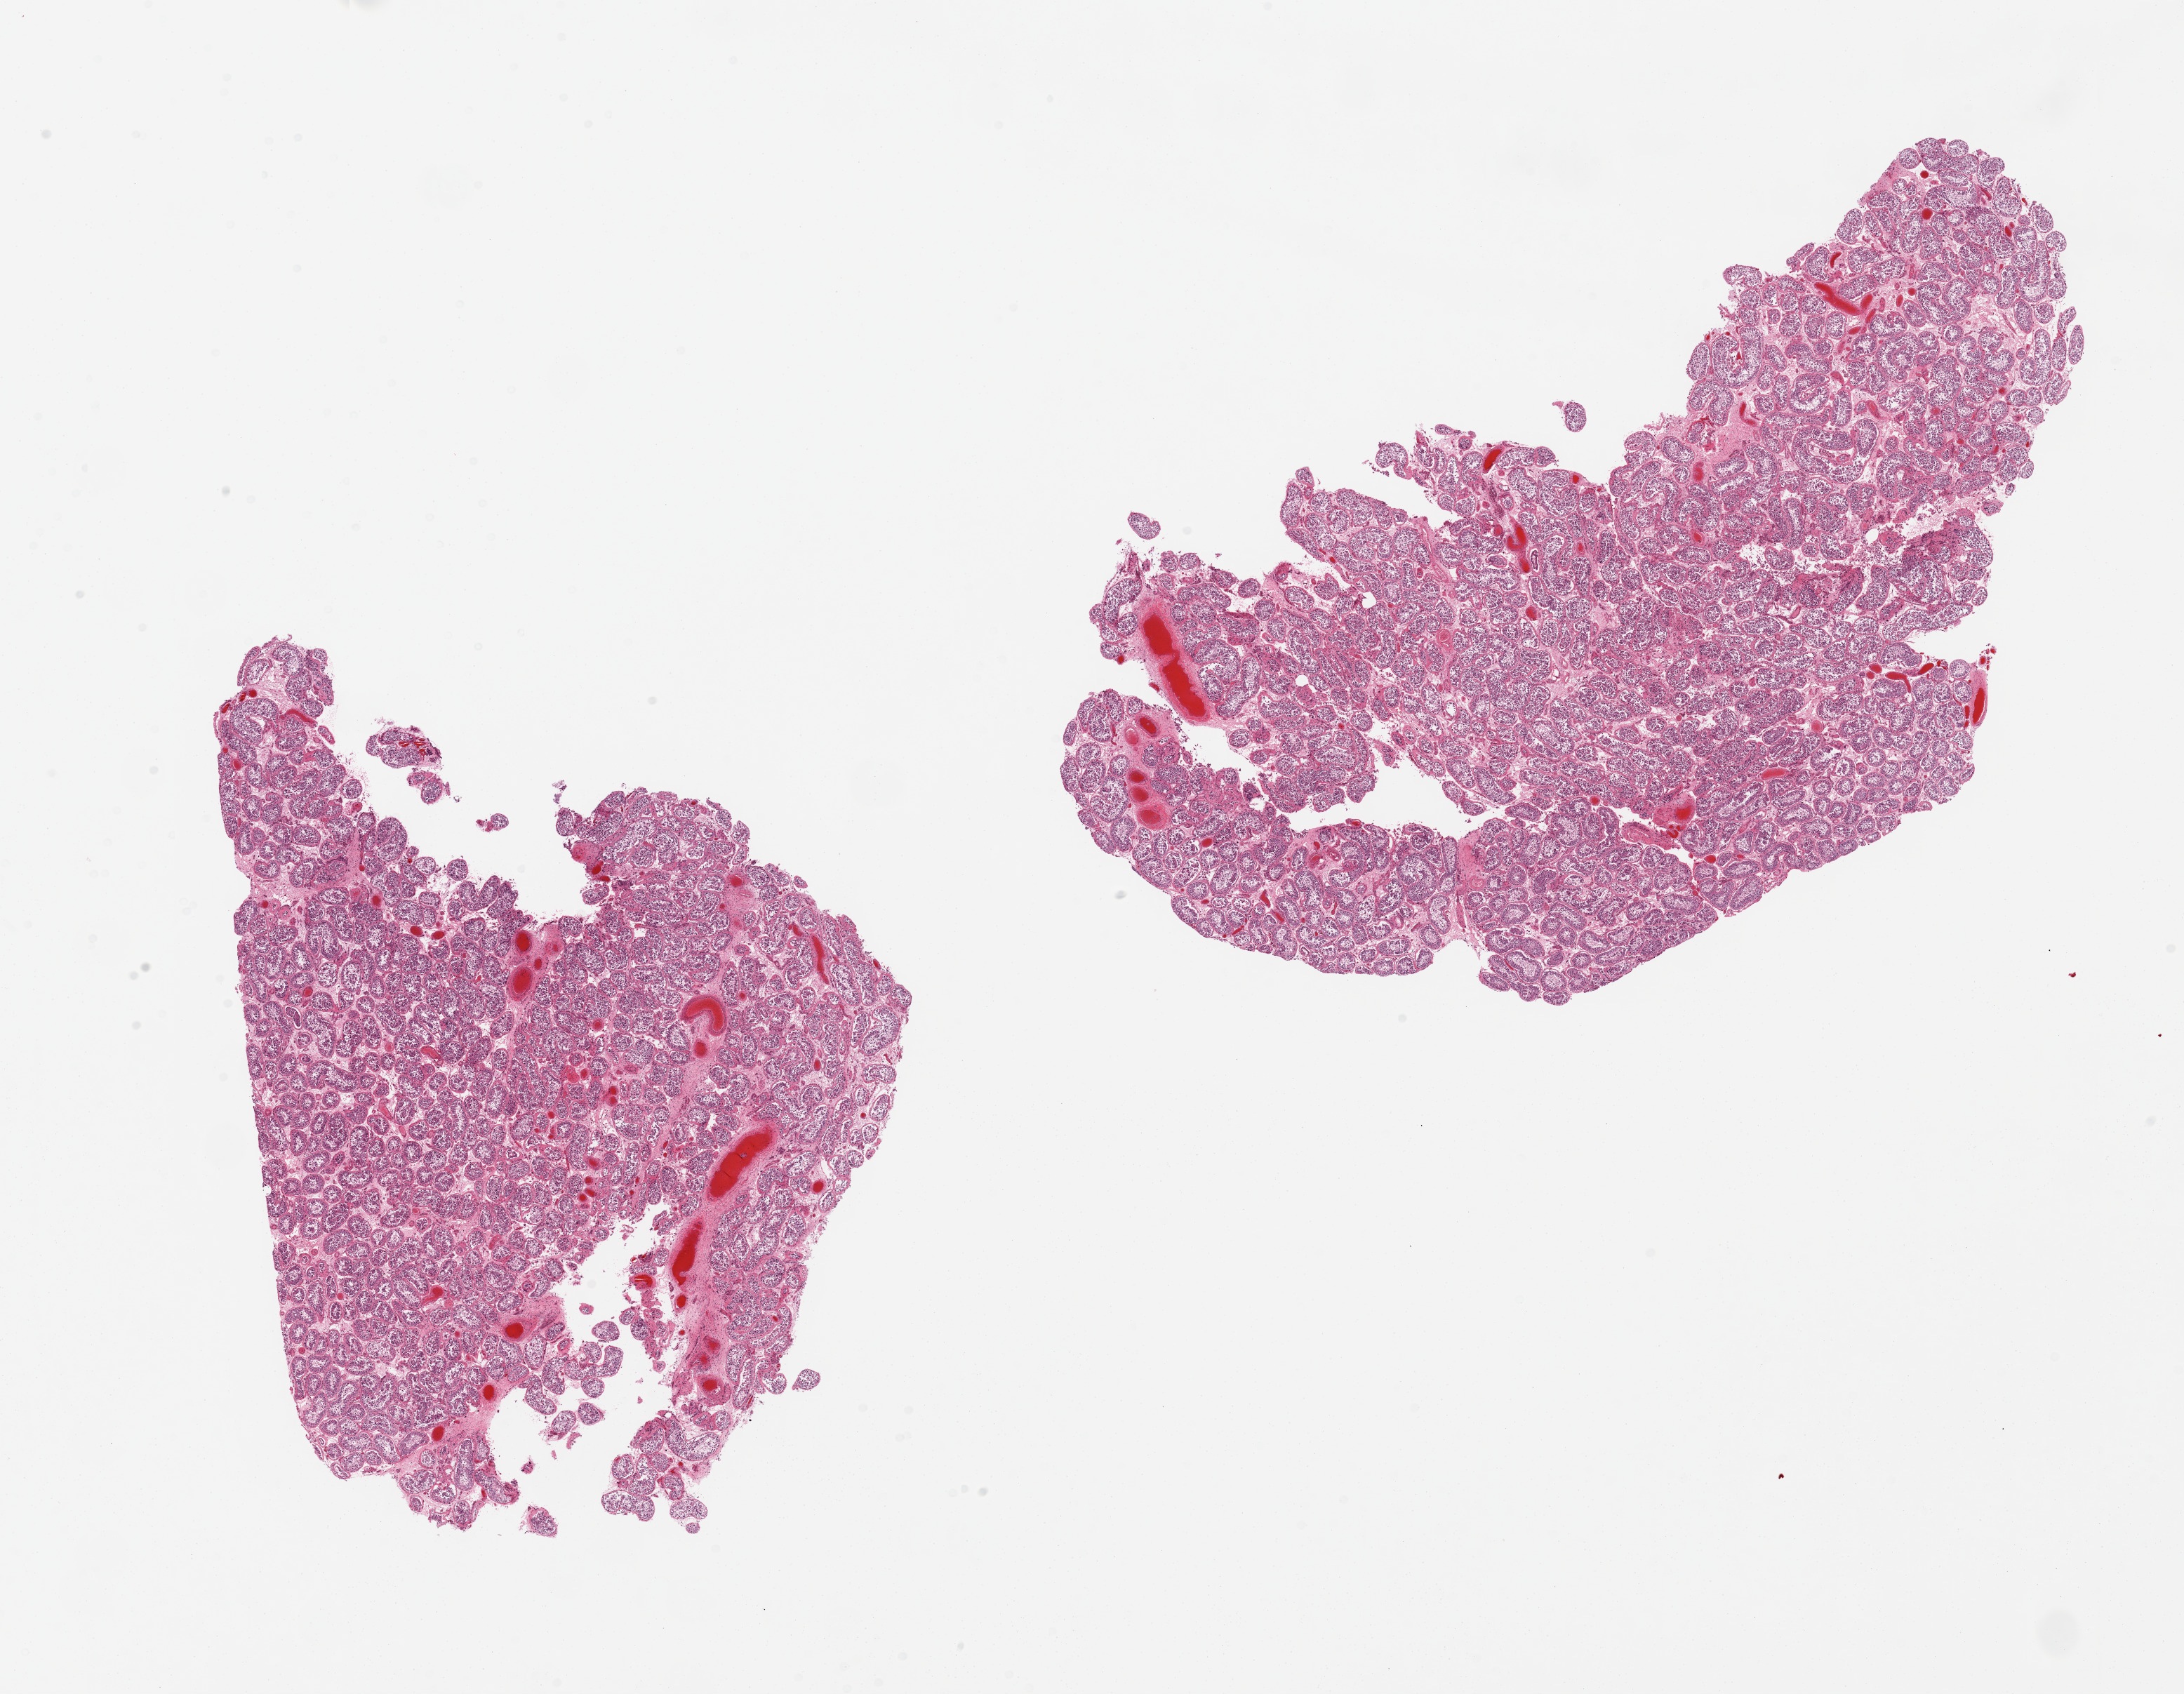
Digitized hematoxylin and eosin (H&E)-stained section — a low-resolution overview of the entire scanned area, about 24.6 x 19.1 mm. PAXgene-fixed paraffin-embedded (PFPE) section. Sampled site (target tissue): testis. Donor tissue sample.
Review note (as recorded): 2 pieces, spermatogenesis present.